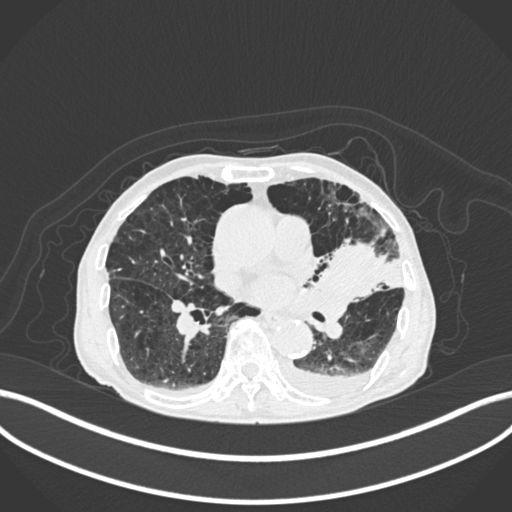
Chest CT, one axial slice. Slice 104 of 400 in the series (ordered by position). Reconstruction kernel B30f. 120 kVp. Lung window (W 1500 / L -600 HU). 1 mm slice thickness. 512 × 512 image matrix. Male patient, age 90 years or older. From the clinical record (not read from this slice): clinical TNM (as recorded): T2b N1 M0.
Outlined on this slice (rectangle marked by the reading radiologist):
- lung tumour (recorded histology: squamous cell carcinoma): box from (x=312, y=236) to (x=389, y=306) px